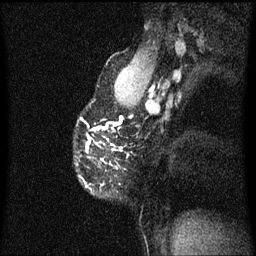
Breast MRI (dynamic contrast-enhanced), one sagittal slice; position 45 of 60 along the scan axis; dynamic contrast-enhanced series, image 2 of 3 at this slice position (ordered by acquisition); 1.5 T; TE 4.2 ms, TR 8.4 ms; 2 mm slice thickness; 256 × 256 image matrix, field of view 200 × 200 mm. Patient: female, 40 years.
Structures marked on this image (semi-automatically segmented with operator editing):
- analysis volume of interest (the breast-tissue region the enhancement analysis was run in; not a lesion): bounding box <80,118,122,189> (left, top, right, bottom; pixels)
- tumour enhancement mask (voxels above the 70 % enhancement threshold inside the analysis volume of interest): <97,128,121,161>